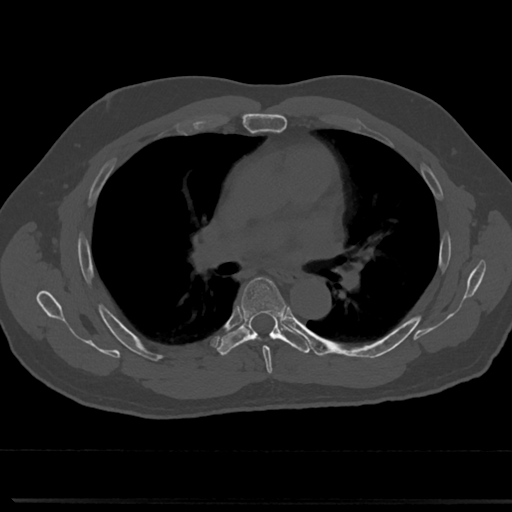
CT including the spine, one axial slice; position 467 of 817 along the scan axis; bone window (W 1800 / L 400 HU); 0.5 mm slice thickness; 512 × 512 image matrix, field of view 355 × 355 mm. Patient: male, 61 years. From the clinical record (not read from this slice): primary cancer: prostate.
Structures marked on this image (semi-automatically segmented with operator editing):
- T5 vertebra: bounding box <242,278,284,363> (left, top, right, bottom; pixels)
- T6 vertebra: <218,275,305,354>